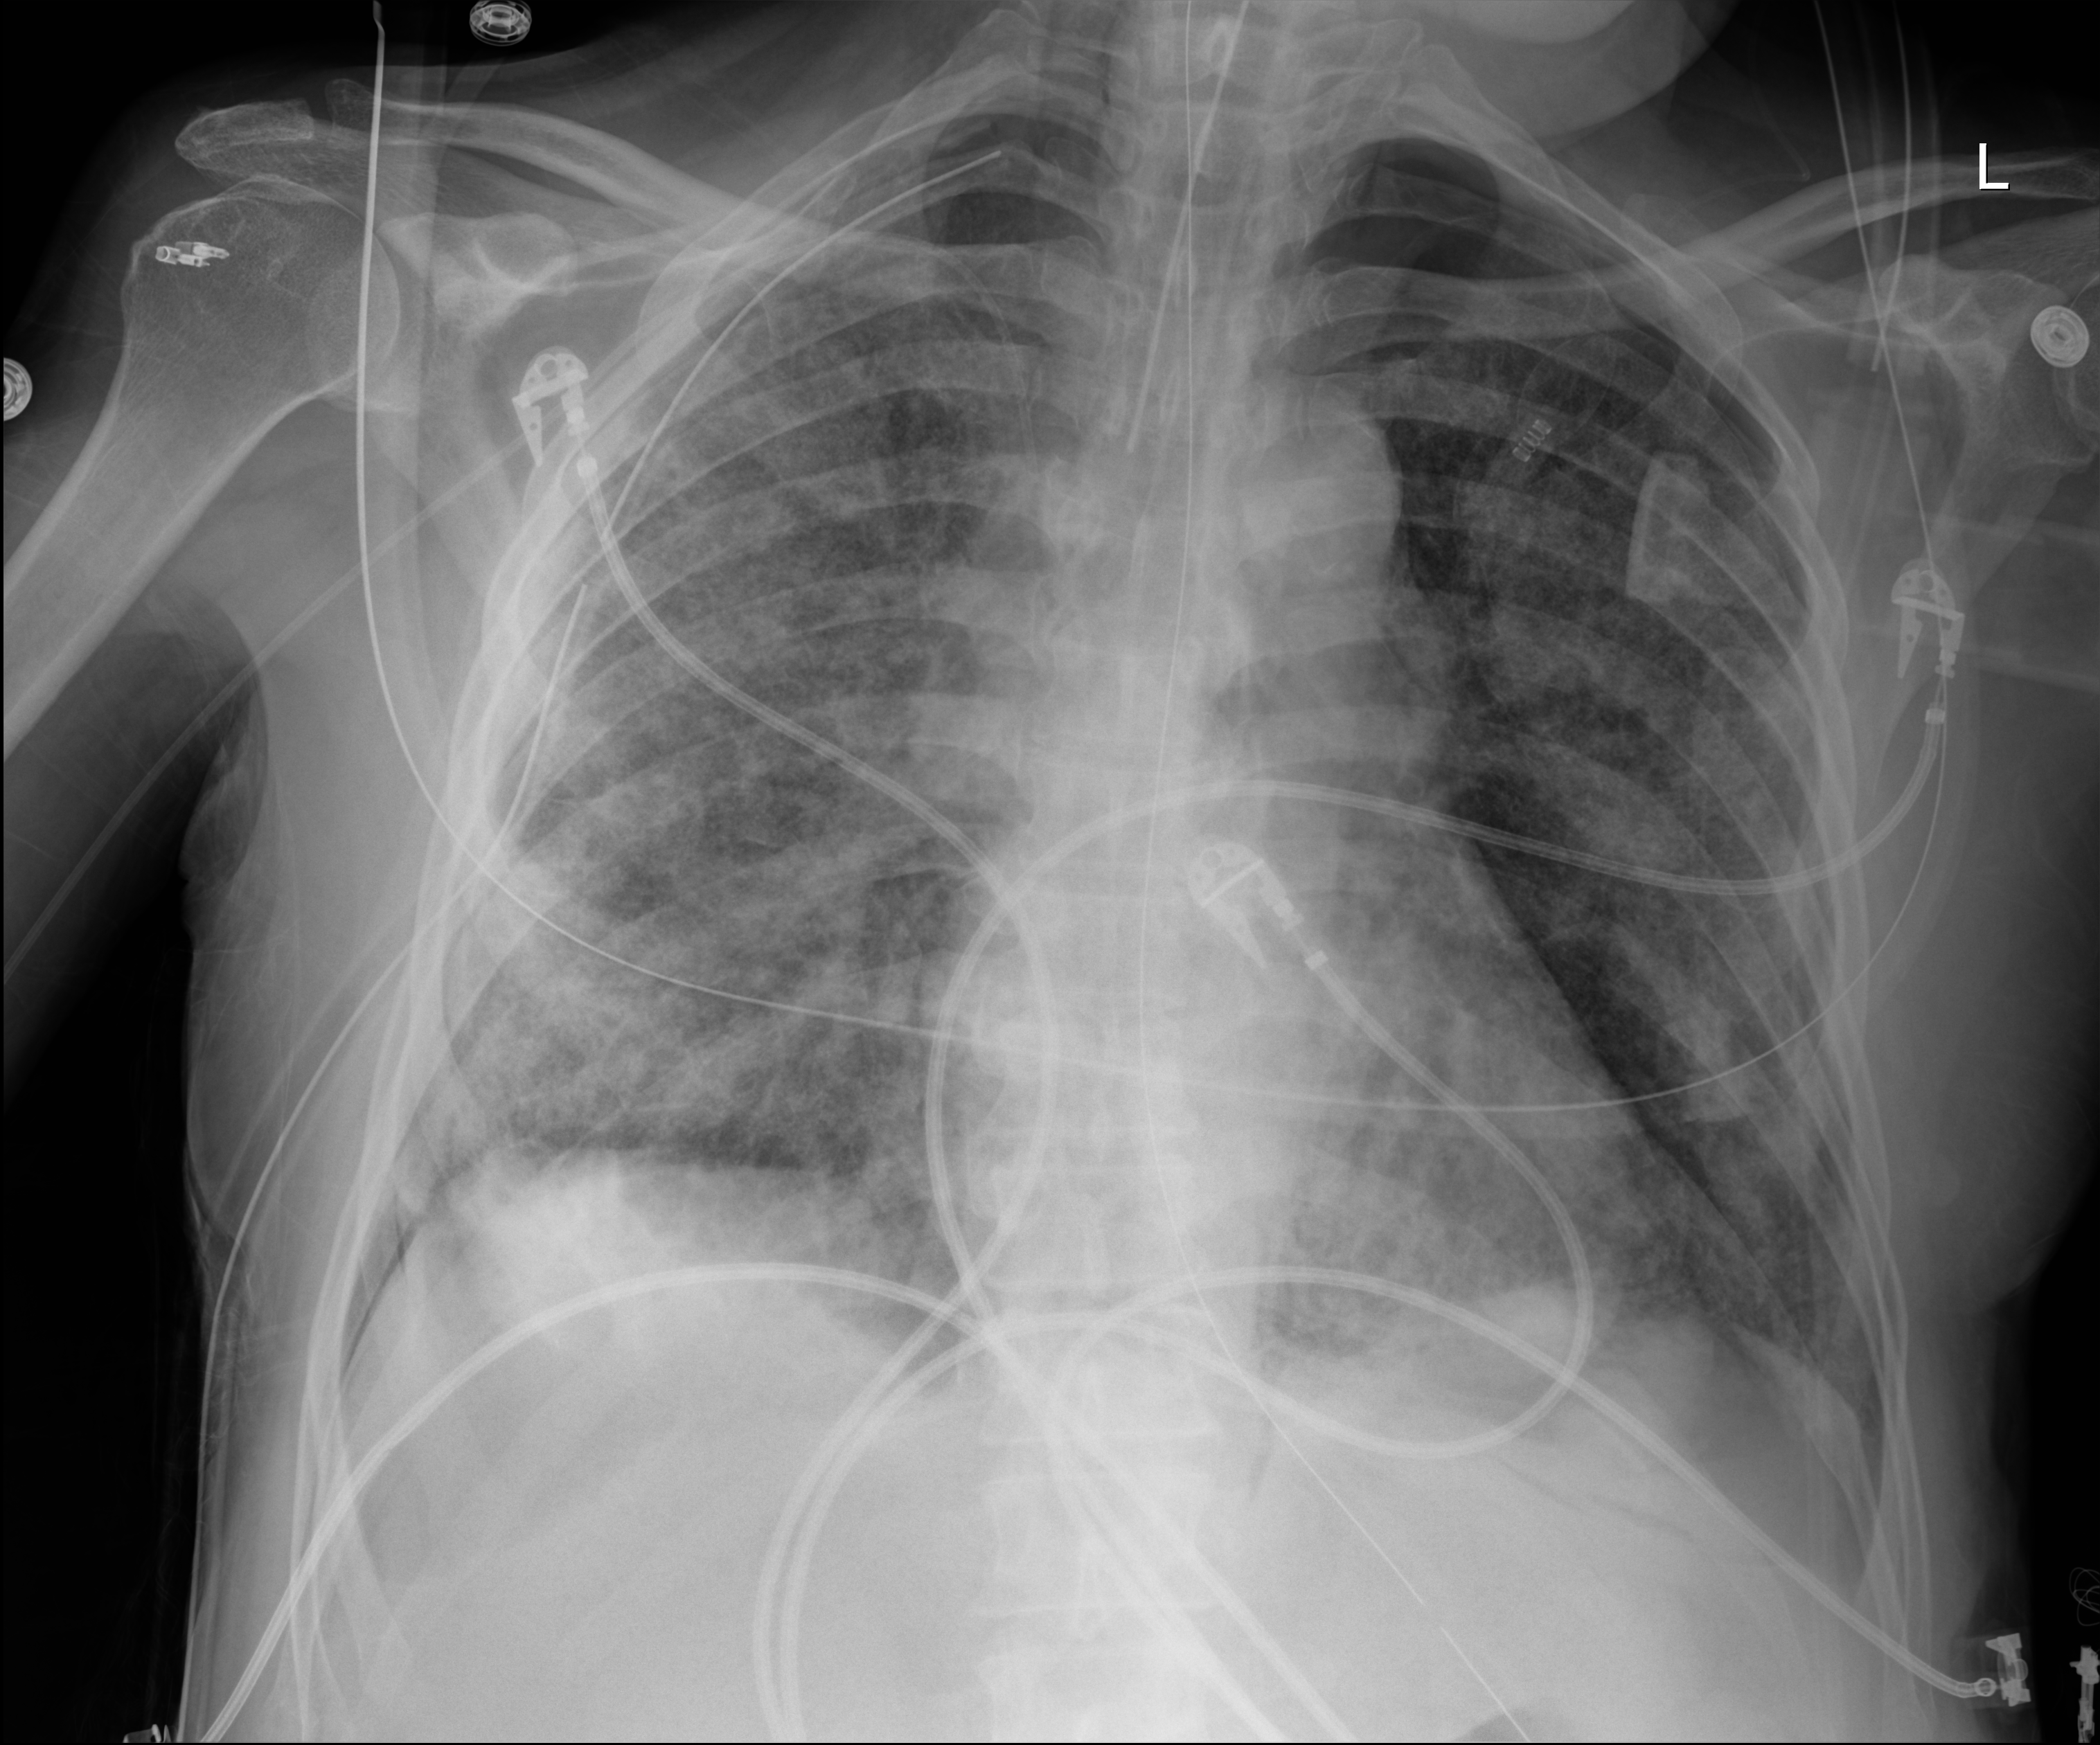
Chest X-ray (portable), anteroposterior (AP) projection. Patient hospitalised with COVID-19; male, aged 60–74 years.
Admission-level facts for this patient (not findings on this image; timing relative to this image not recorded):
- chronic kidney disease (admission record): no